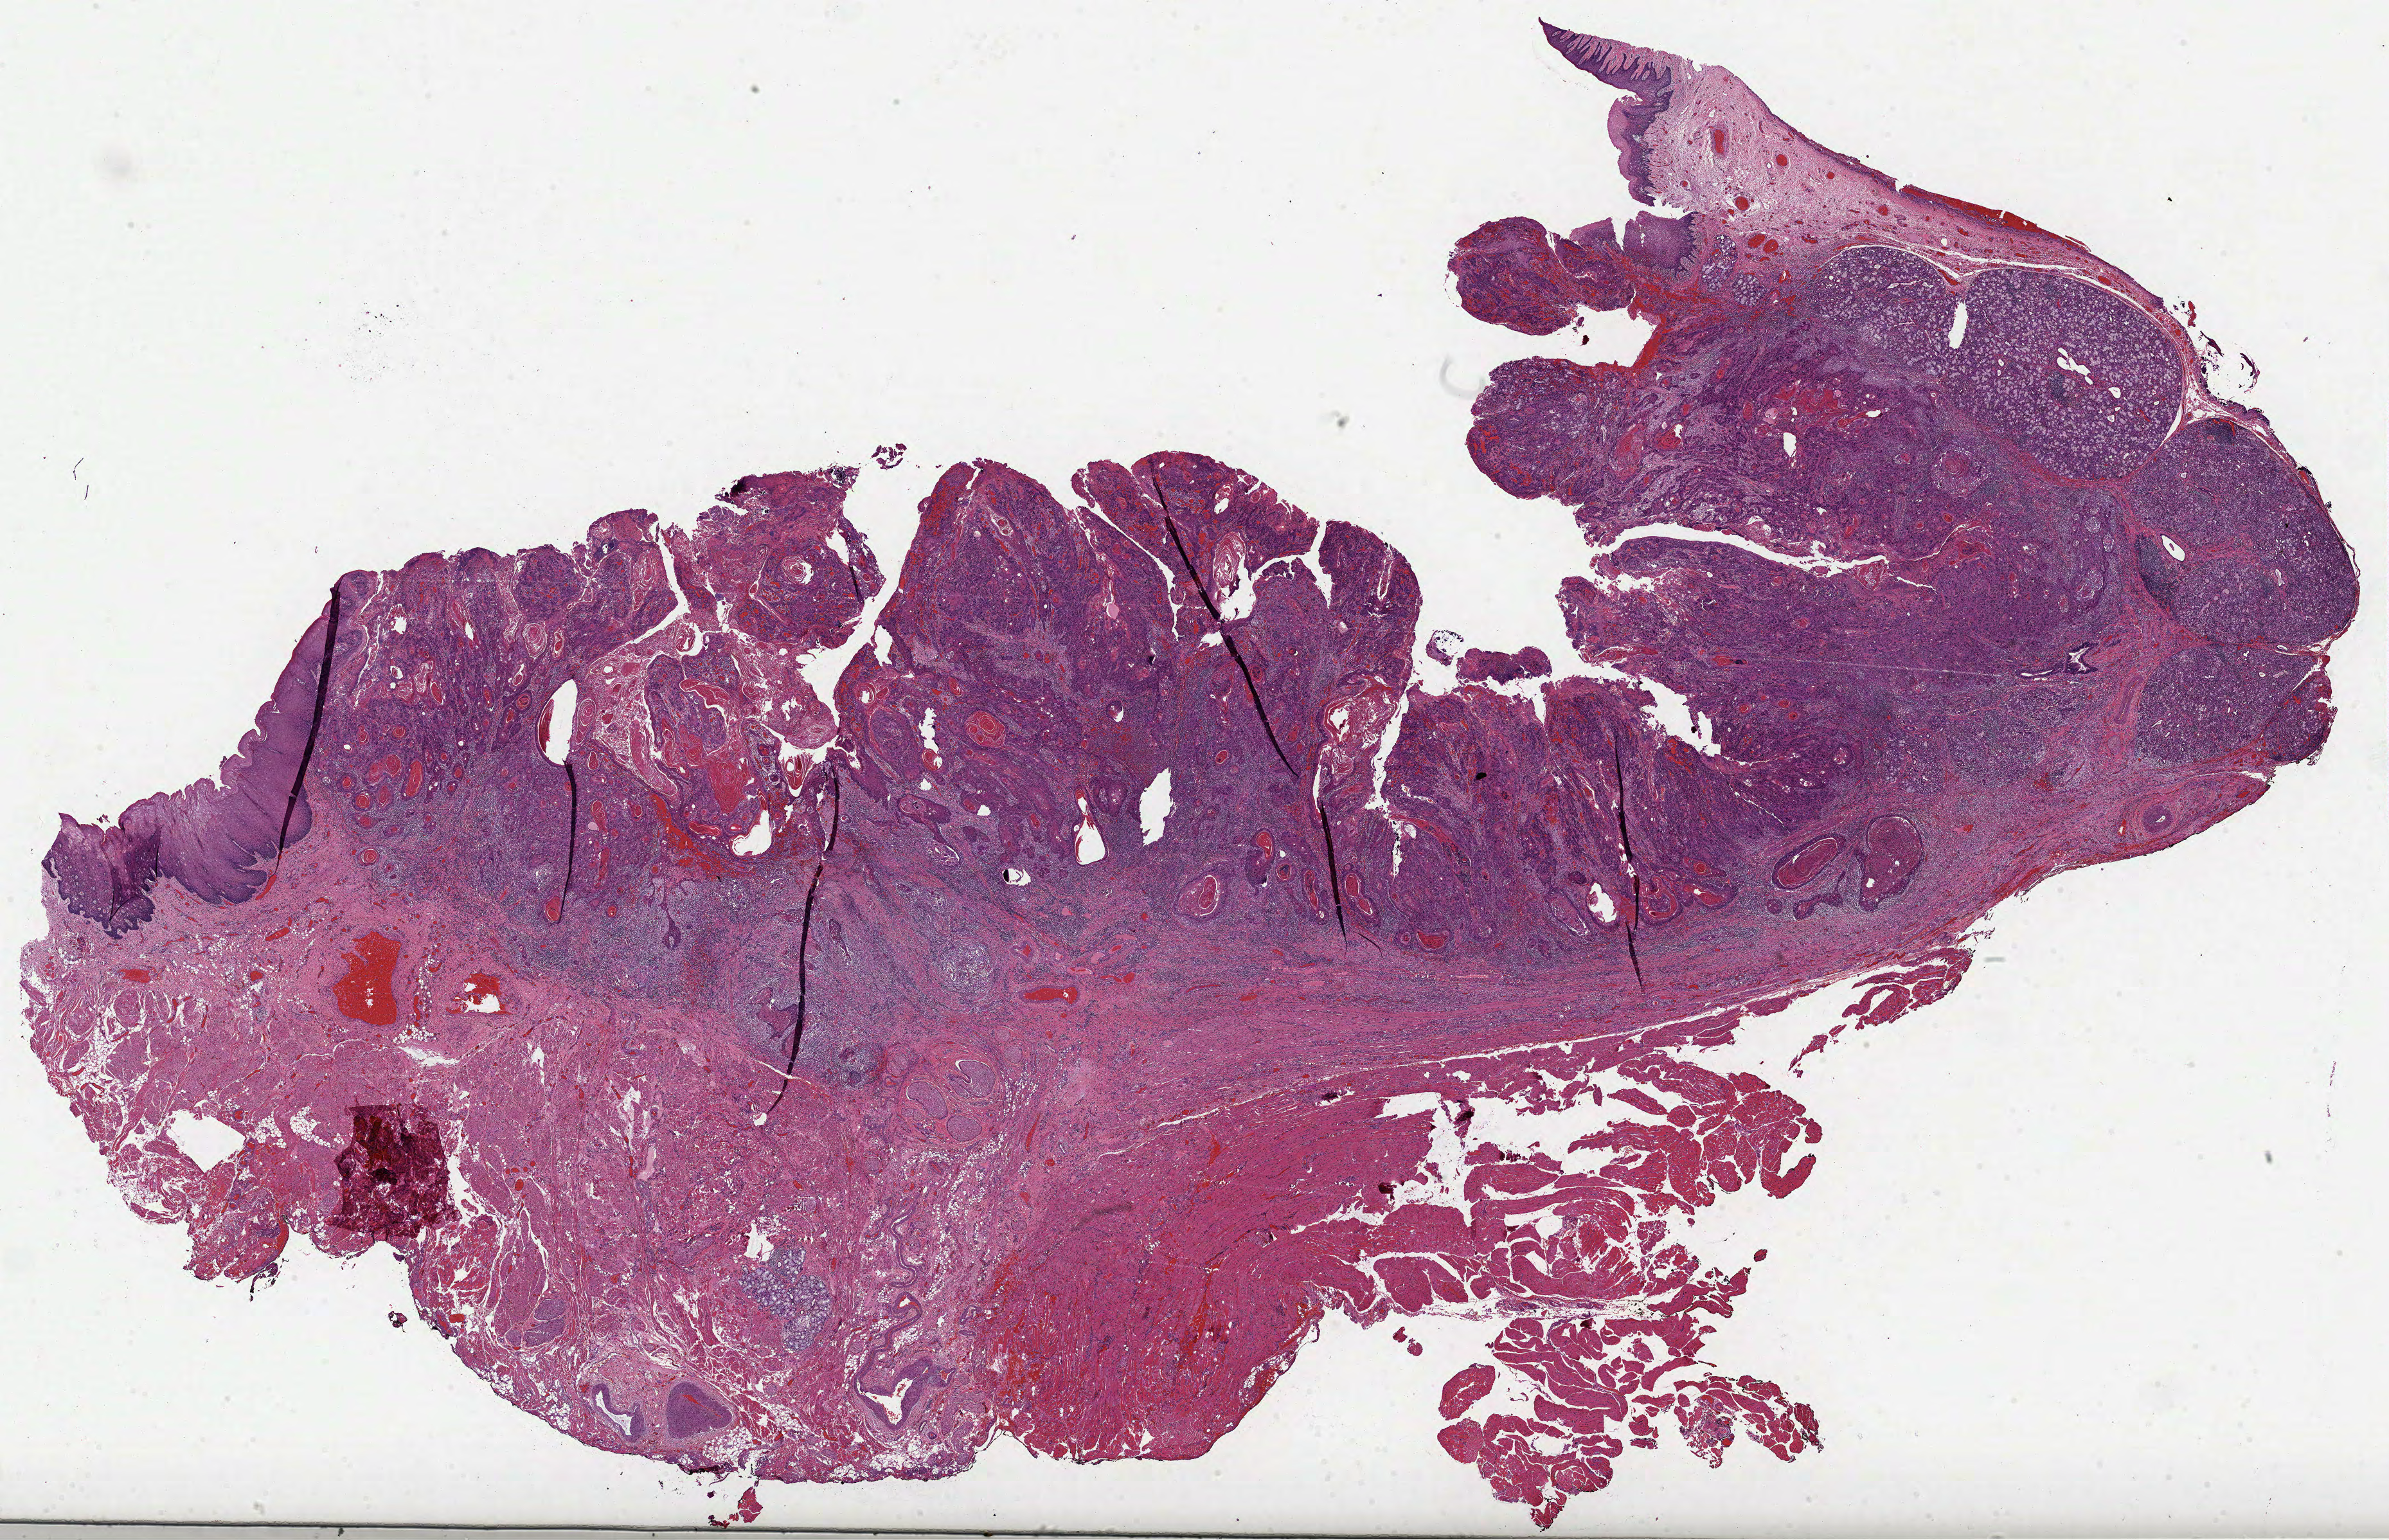
H&E whole-slide image — low-resolution overview of the scanned area, about 30.0 x 19.3 mm (slide scanned at 40x); formalin-fixed paraffin-embedded (FFPE) diagnostic section; head and neck, primary tumour sample. Male patient; age at initial diagnosis 60 years. Histologic grade: G2 (moderately differentiated).
Diagnosis: Squamous cell carcinoma, NOS (floor of mouth, NOS). AJCC pathologic stage: II (7th edition).